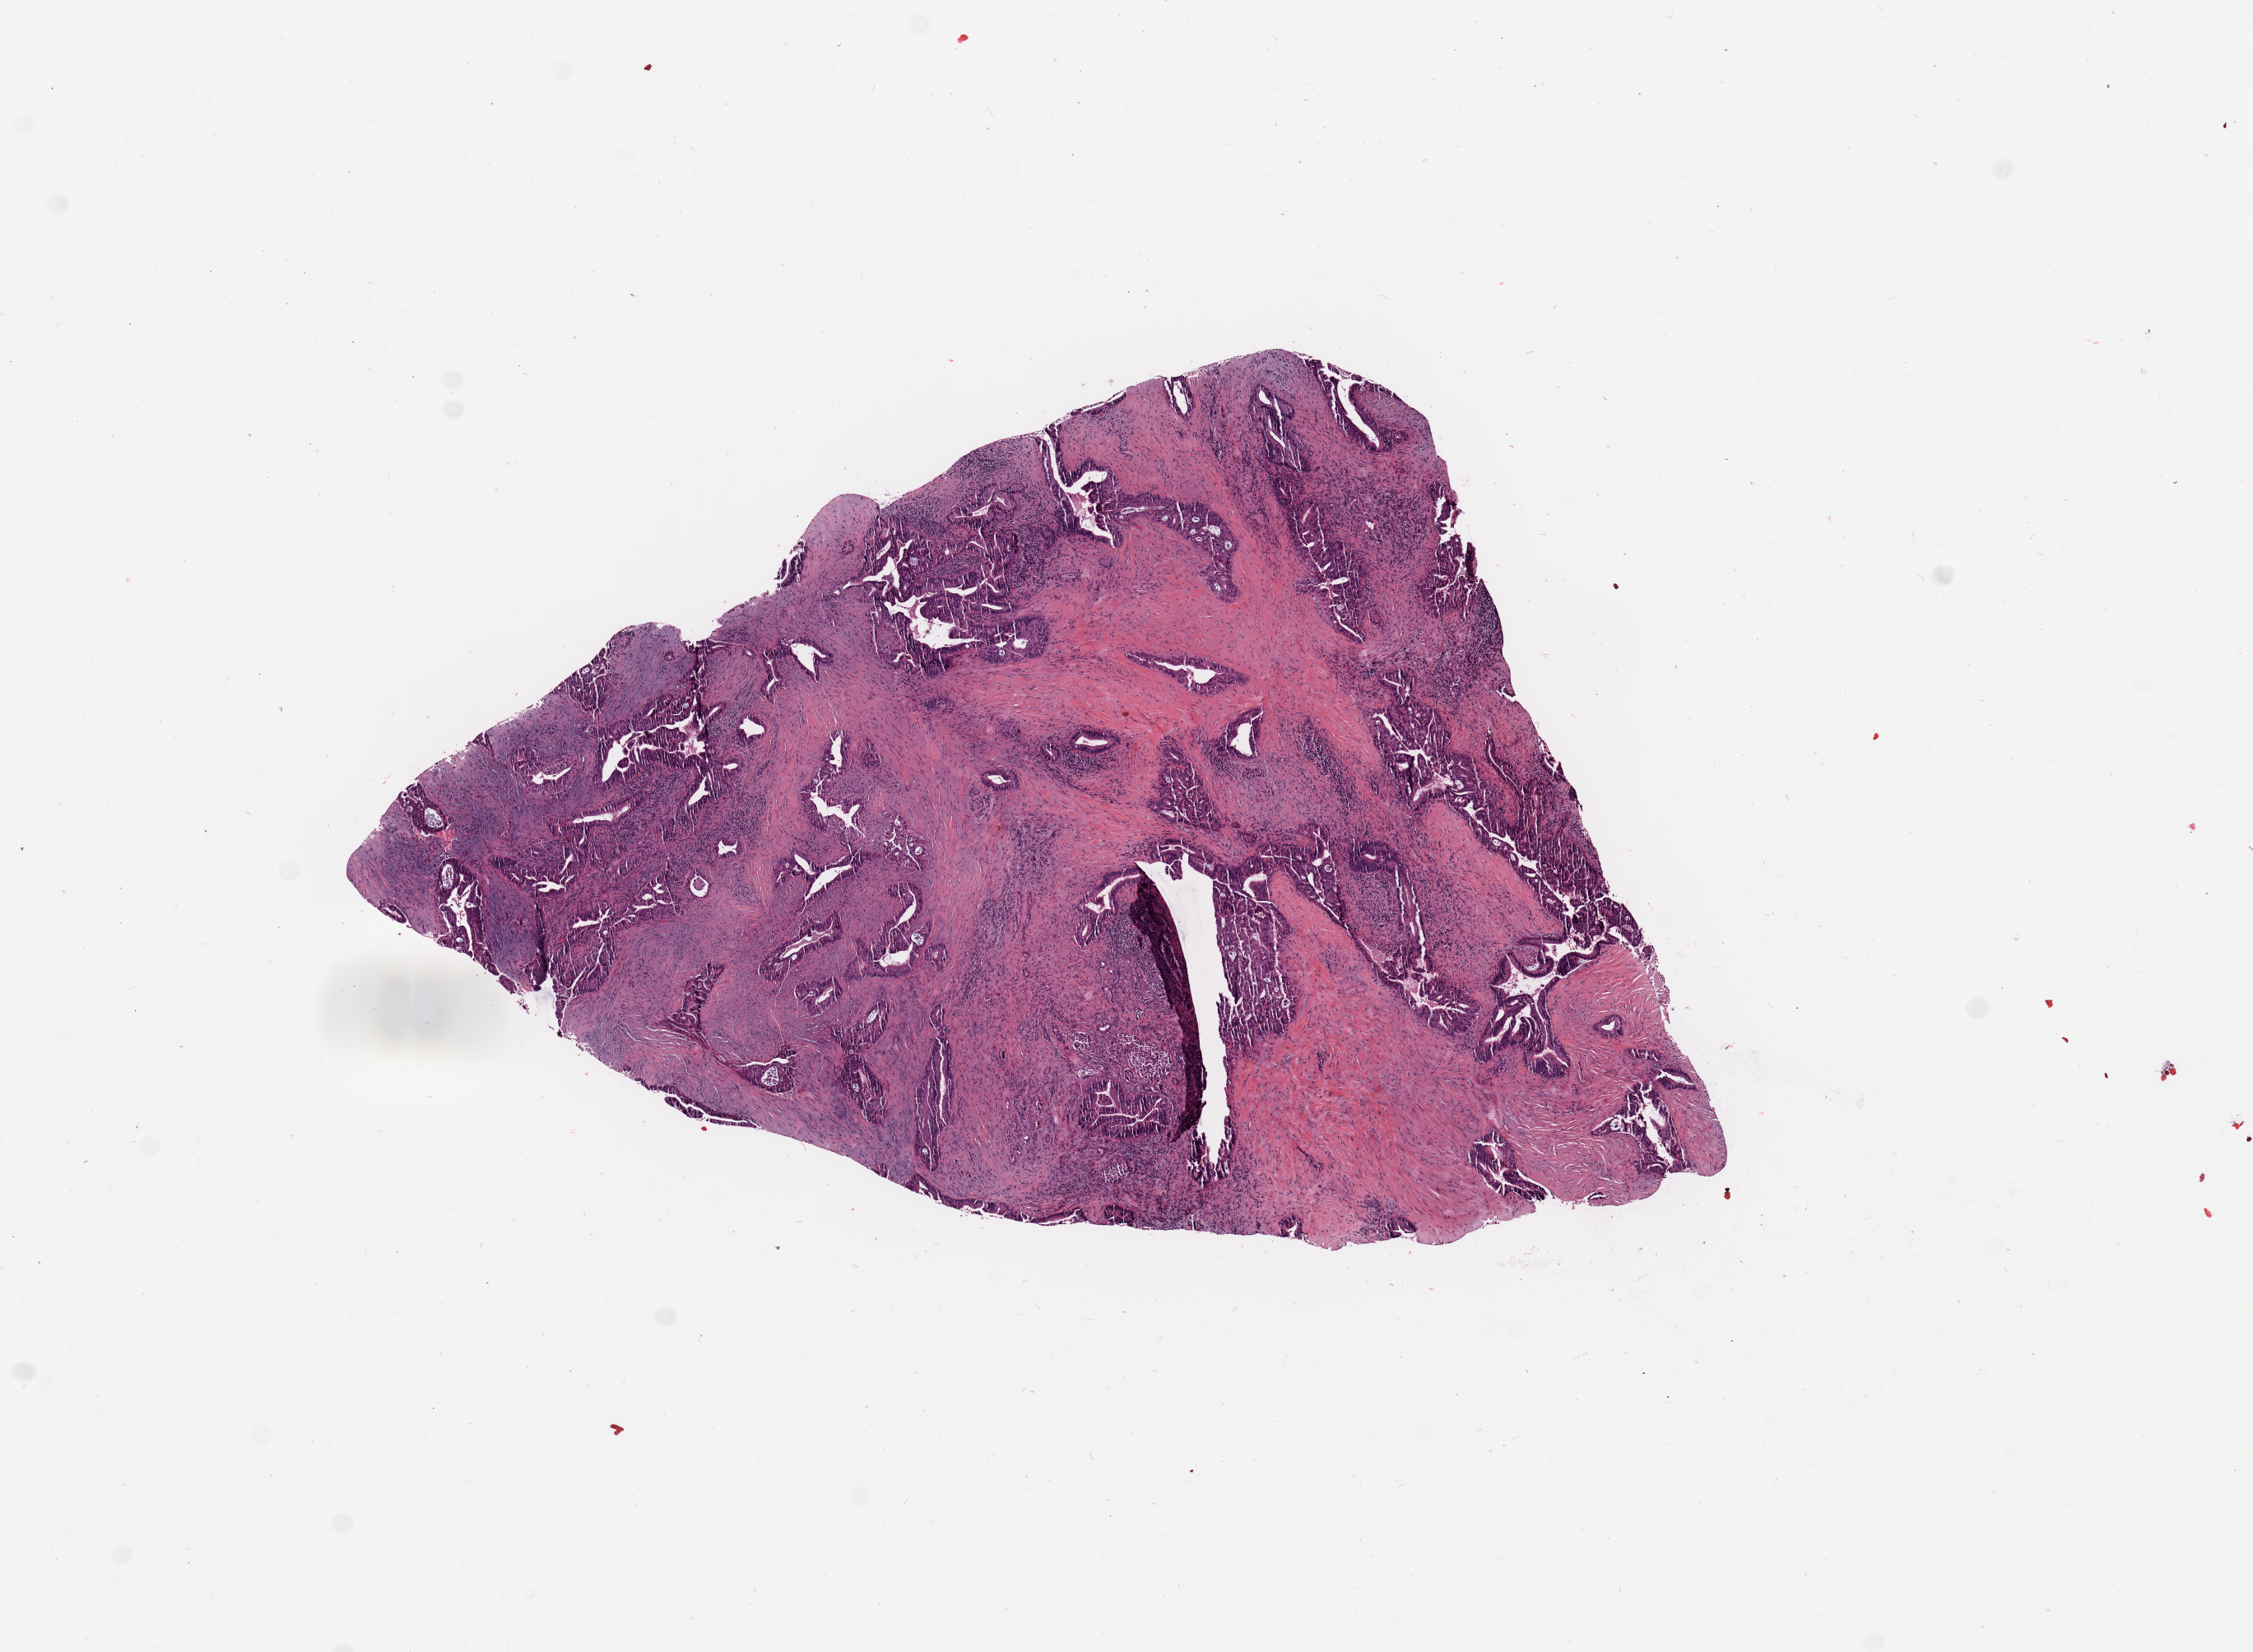
H&E whole-slide image — whole scanned area (about 10.8 x 7.9 mm, from a 20x scan) shown as a low-resolution overview, tumour tissue sample, sampled site: pancreas. 63-year-old male patient. Histologic grade: G2 (moderately differentiated). Pathologist review of this section (percent, as recorded): tumour nuclei 60%, necrosis 0%.
AJCC pathologic stage: IB. Primary tumour site (as recorded): head. Diagnosis: Infiltrating duct carcinoma, NOS.